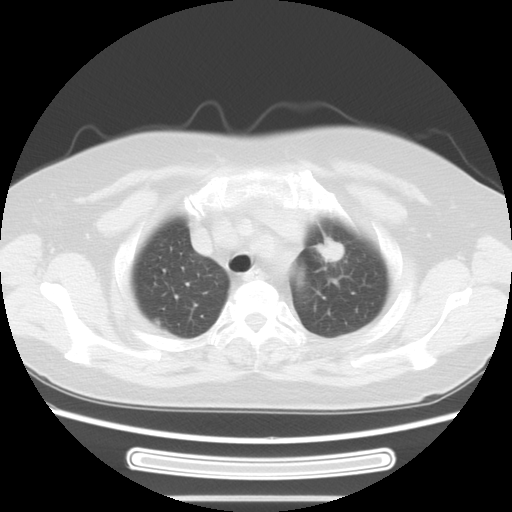
Chest CT, one axial slice; position 48 of 58 along the scan axis; lung window (W 1500 / L -600 HU); 5 mm slice thickness; 512 × 512 image matrix. Female patient, age 70 years. From the clinical record (not read from this slice): clinical TNM (as recorded): T1c N0 M0; histopathological grade: G2-3.
Annotated regions visible in this slice (bounding box drawn by a radiologist):
- lung tumour (recorded histology: adenocarcinoma): bounding box [x1, y1, x2, y2] px = [304, 227, 349, 270]